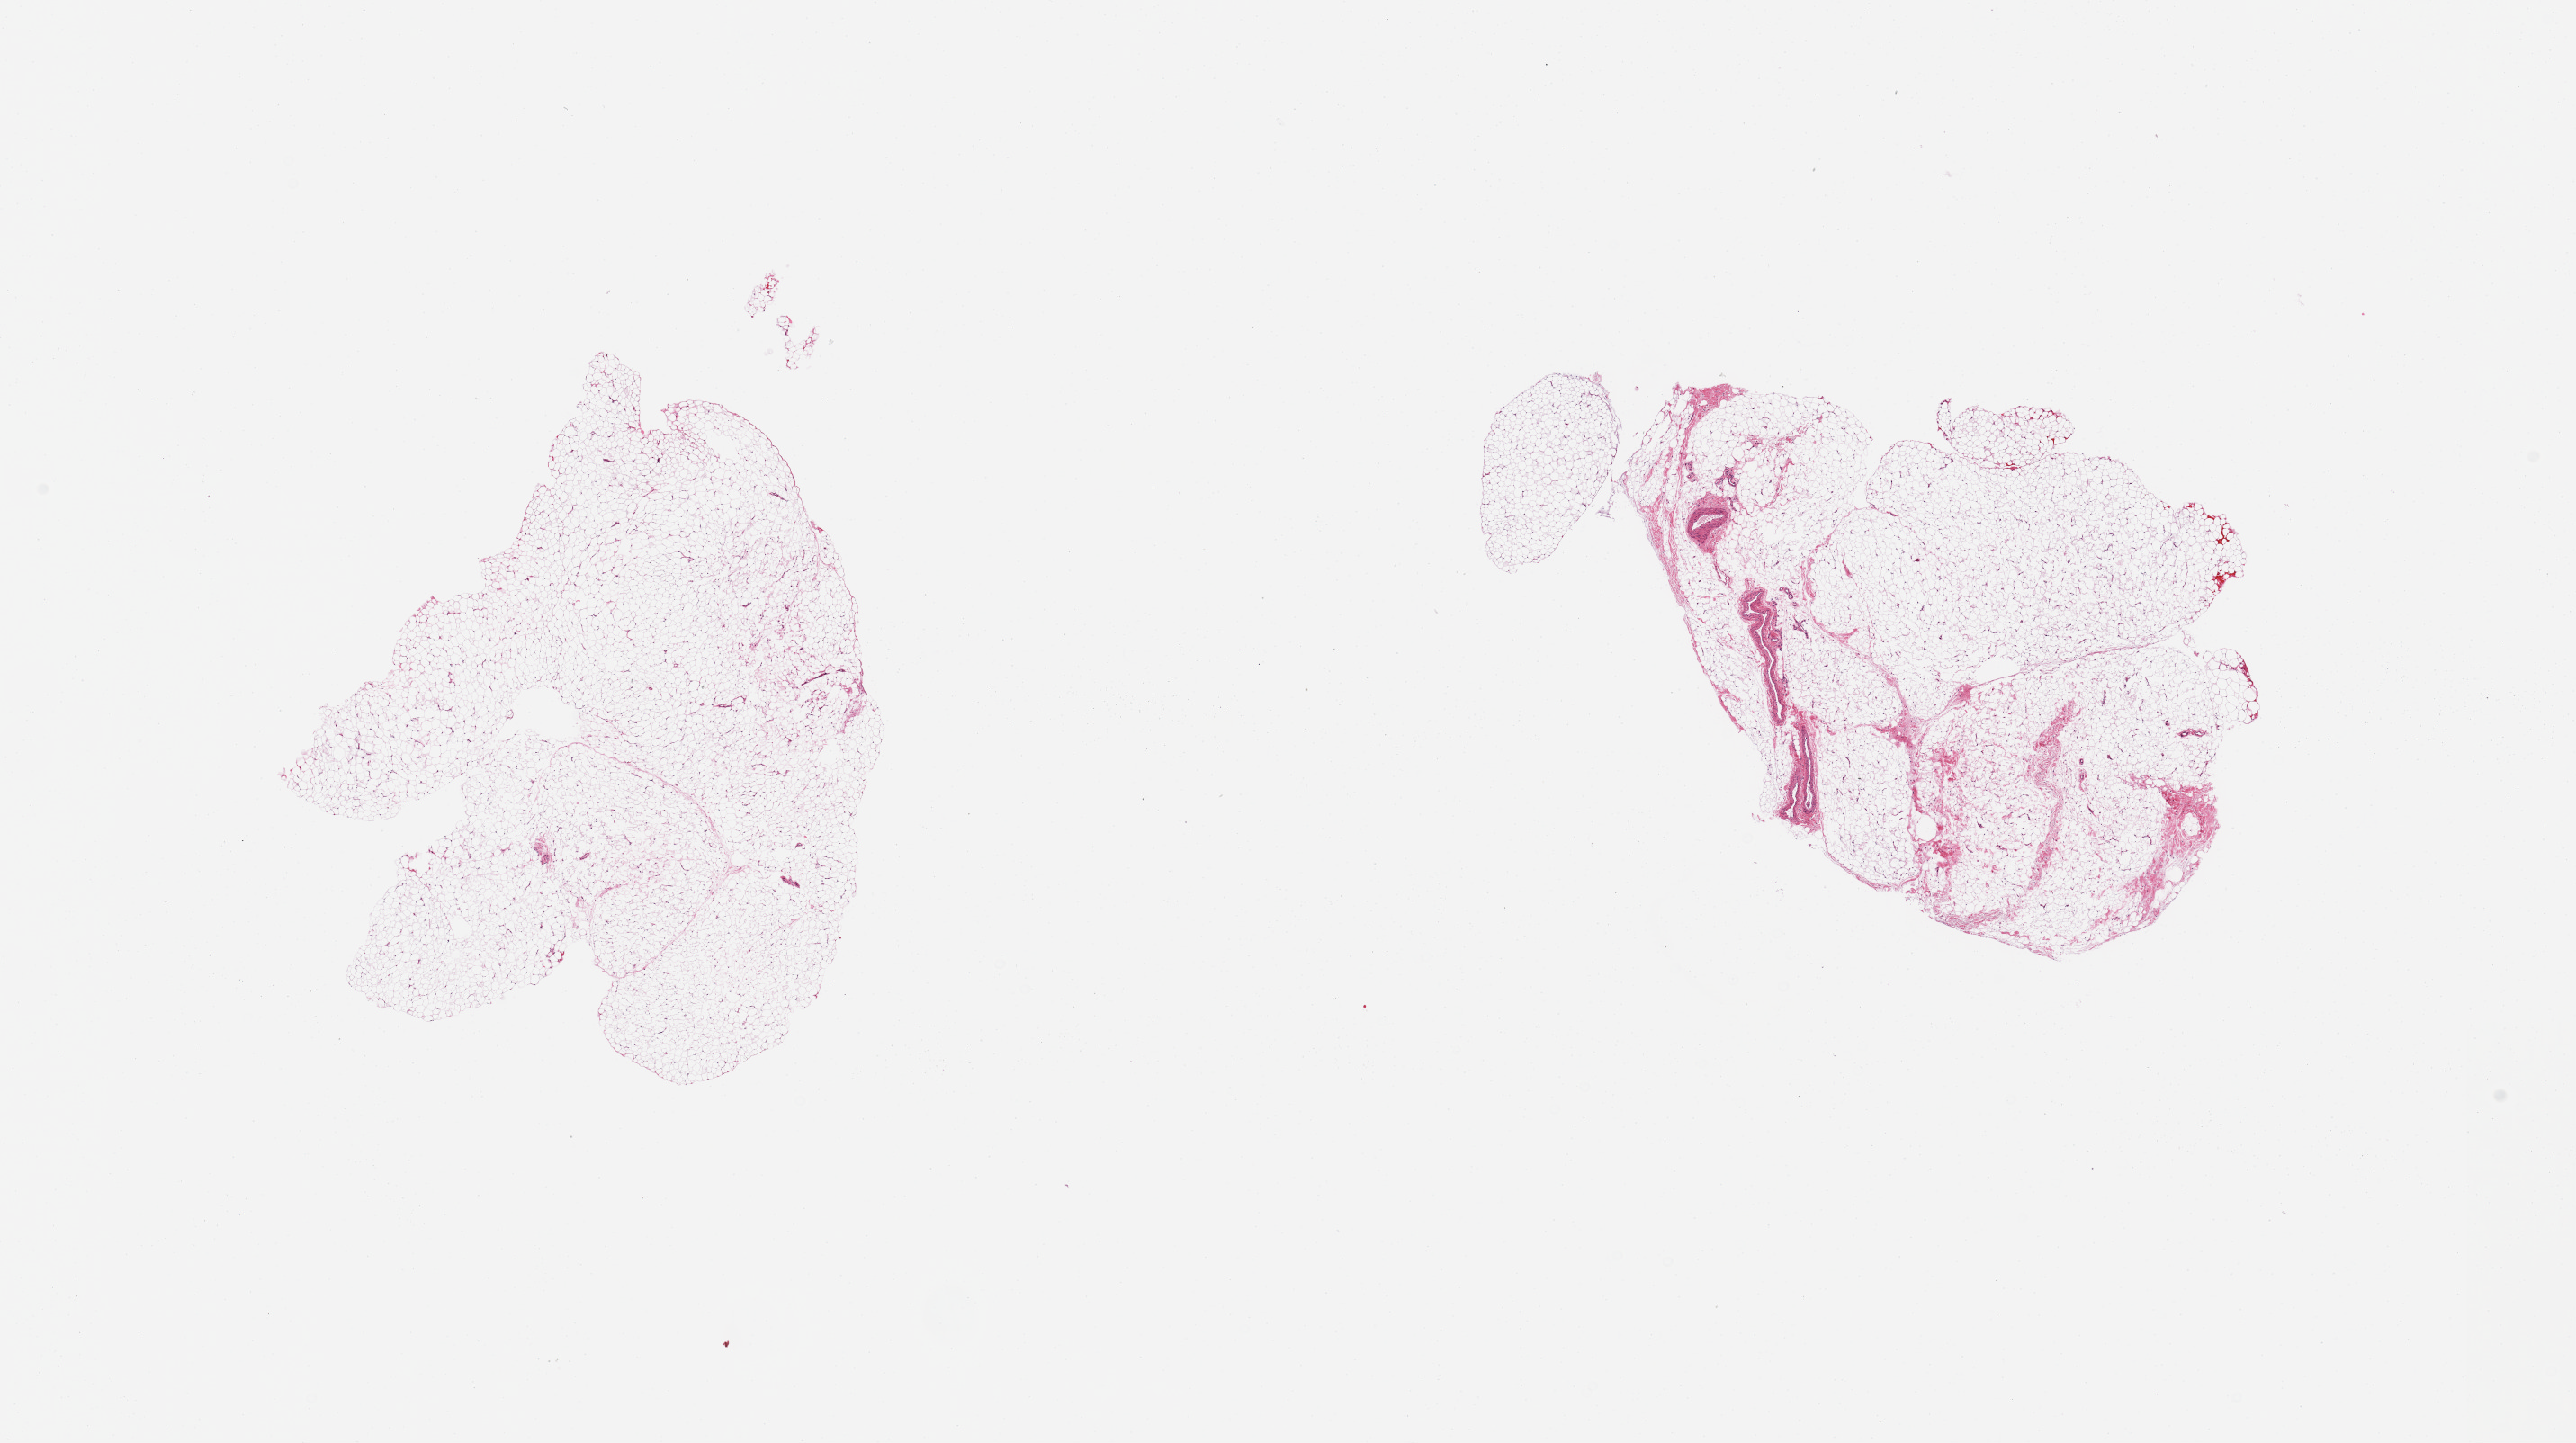
Hematoxylin and eosin (H&E) whole-slide image, whole scanned area (about 22.6 x 12.7 mm, acquisition: 20x scan) shown as a low-resolution overview, PAXgene-fixed paraffin-embedded (PFPE) section, section of adipose tissue (target tissue), donor tissue sample. Donor sex: female.
Pathologist's review note for this sample: 2 pieces, trace vascular elements.